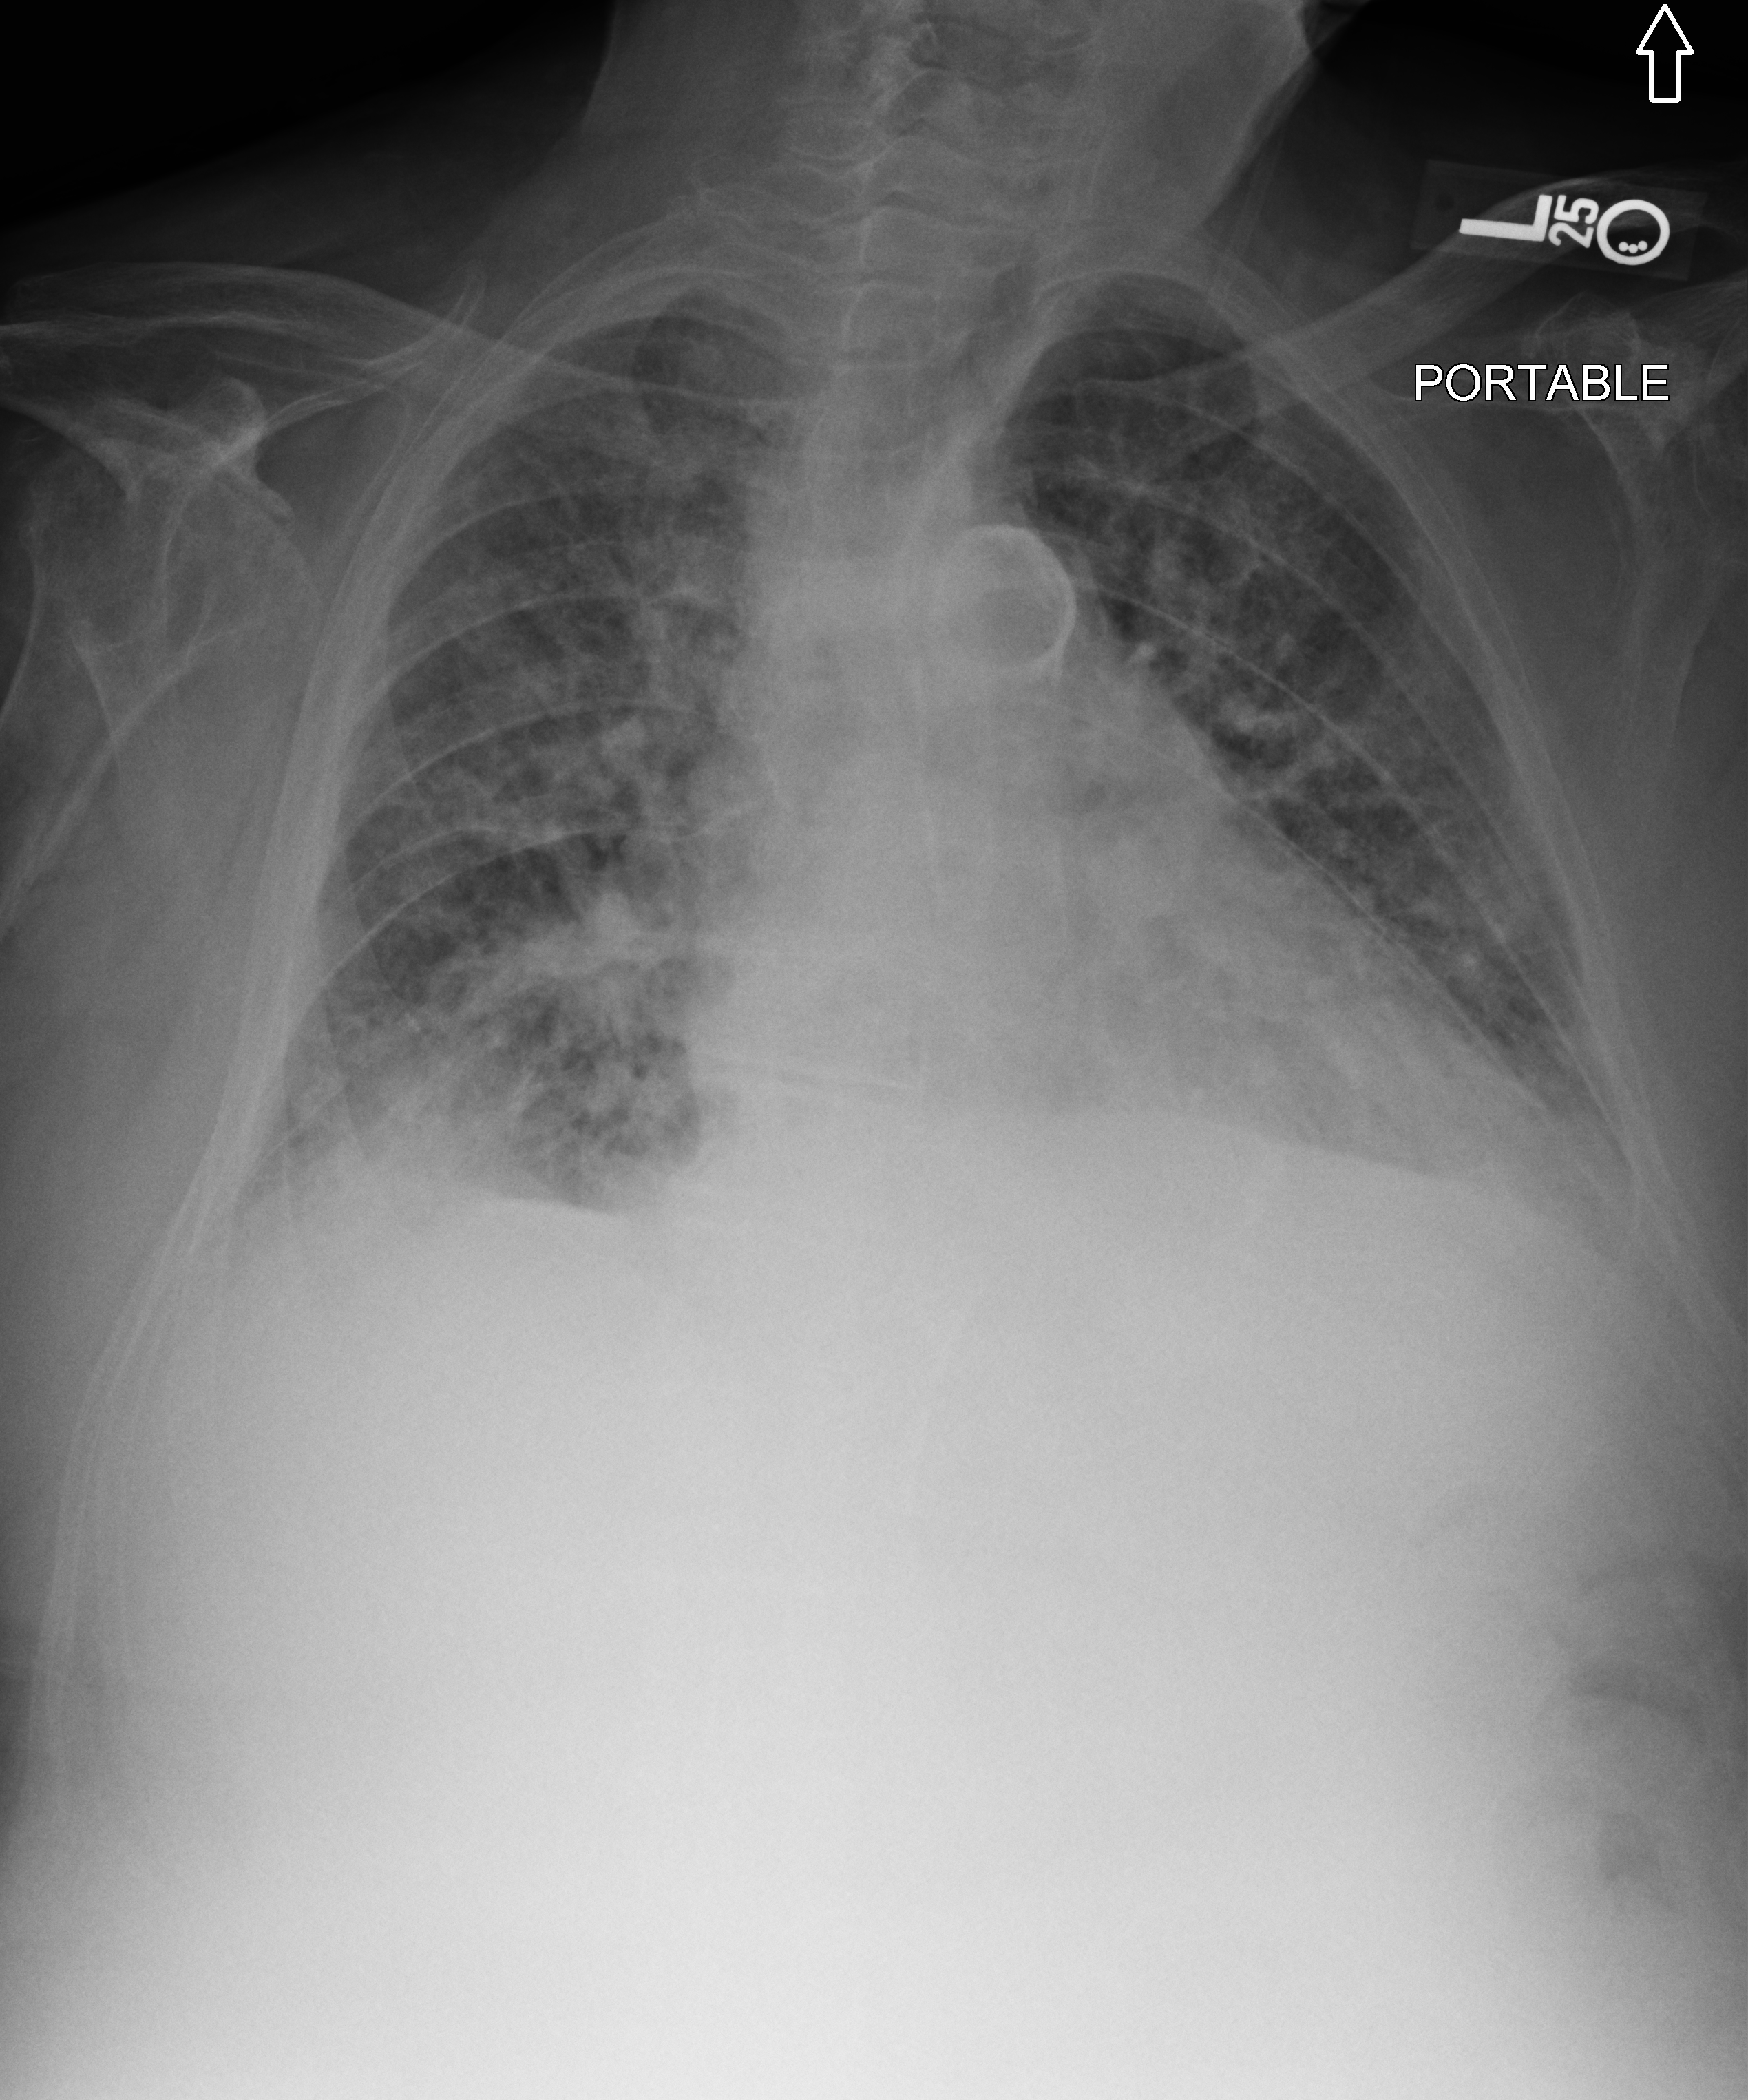
Portable chest radiograph; anteroposterior (AP) projection. Male patient hospitalised with COVID-19, age 75–90 years.
Hospital-stay facts (about this admission, not read from this image; timing relative to this image not recorded):
- admitted to intensive care during this hospital stay: no